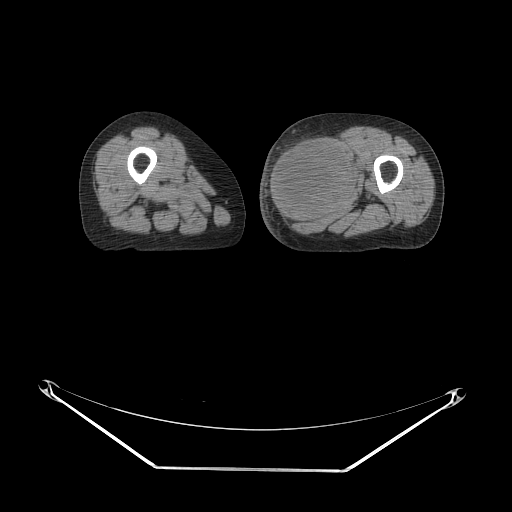
CT of an extremity soft-tissue mass (from a PET/CT study), one axial slice. Position 27 of 91 along the scan axis. 140 kVp. Soft-tissue window (W 400 / L 40 HU). 3.75 mm slice thickness. 512 × 512 image matrix. Female patient. From the clinical record (not read from this slice): histological type: pleomorphic leiomyosarcoma; grade: high; site of the primary tumour: left thigh.
Annotated regions visible in this slice (expert contour drawn on MRI and transferred to this co-registered scan by the dataset authors):
- gross tumour volume including surrounding oedema: bounding box (x1, y1, x2, y2) in pixels: (269, 133, 357, 222)
- gross tumour volume (mass): (269, 135, 355, 222)